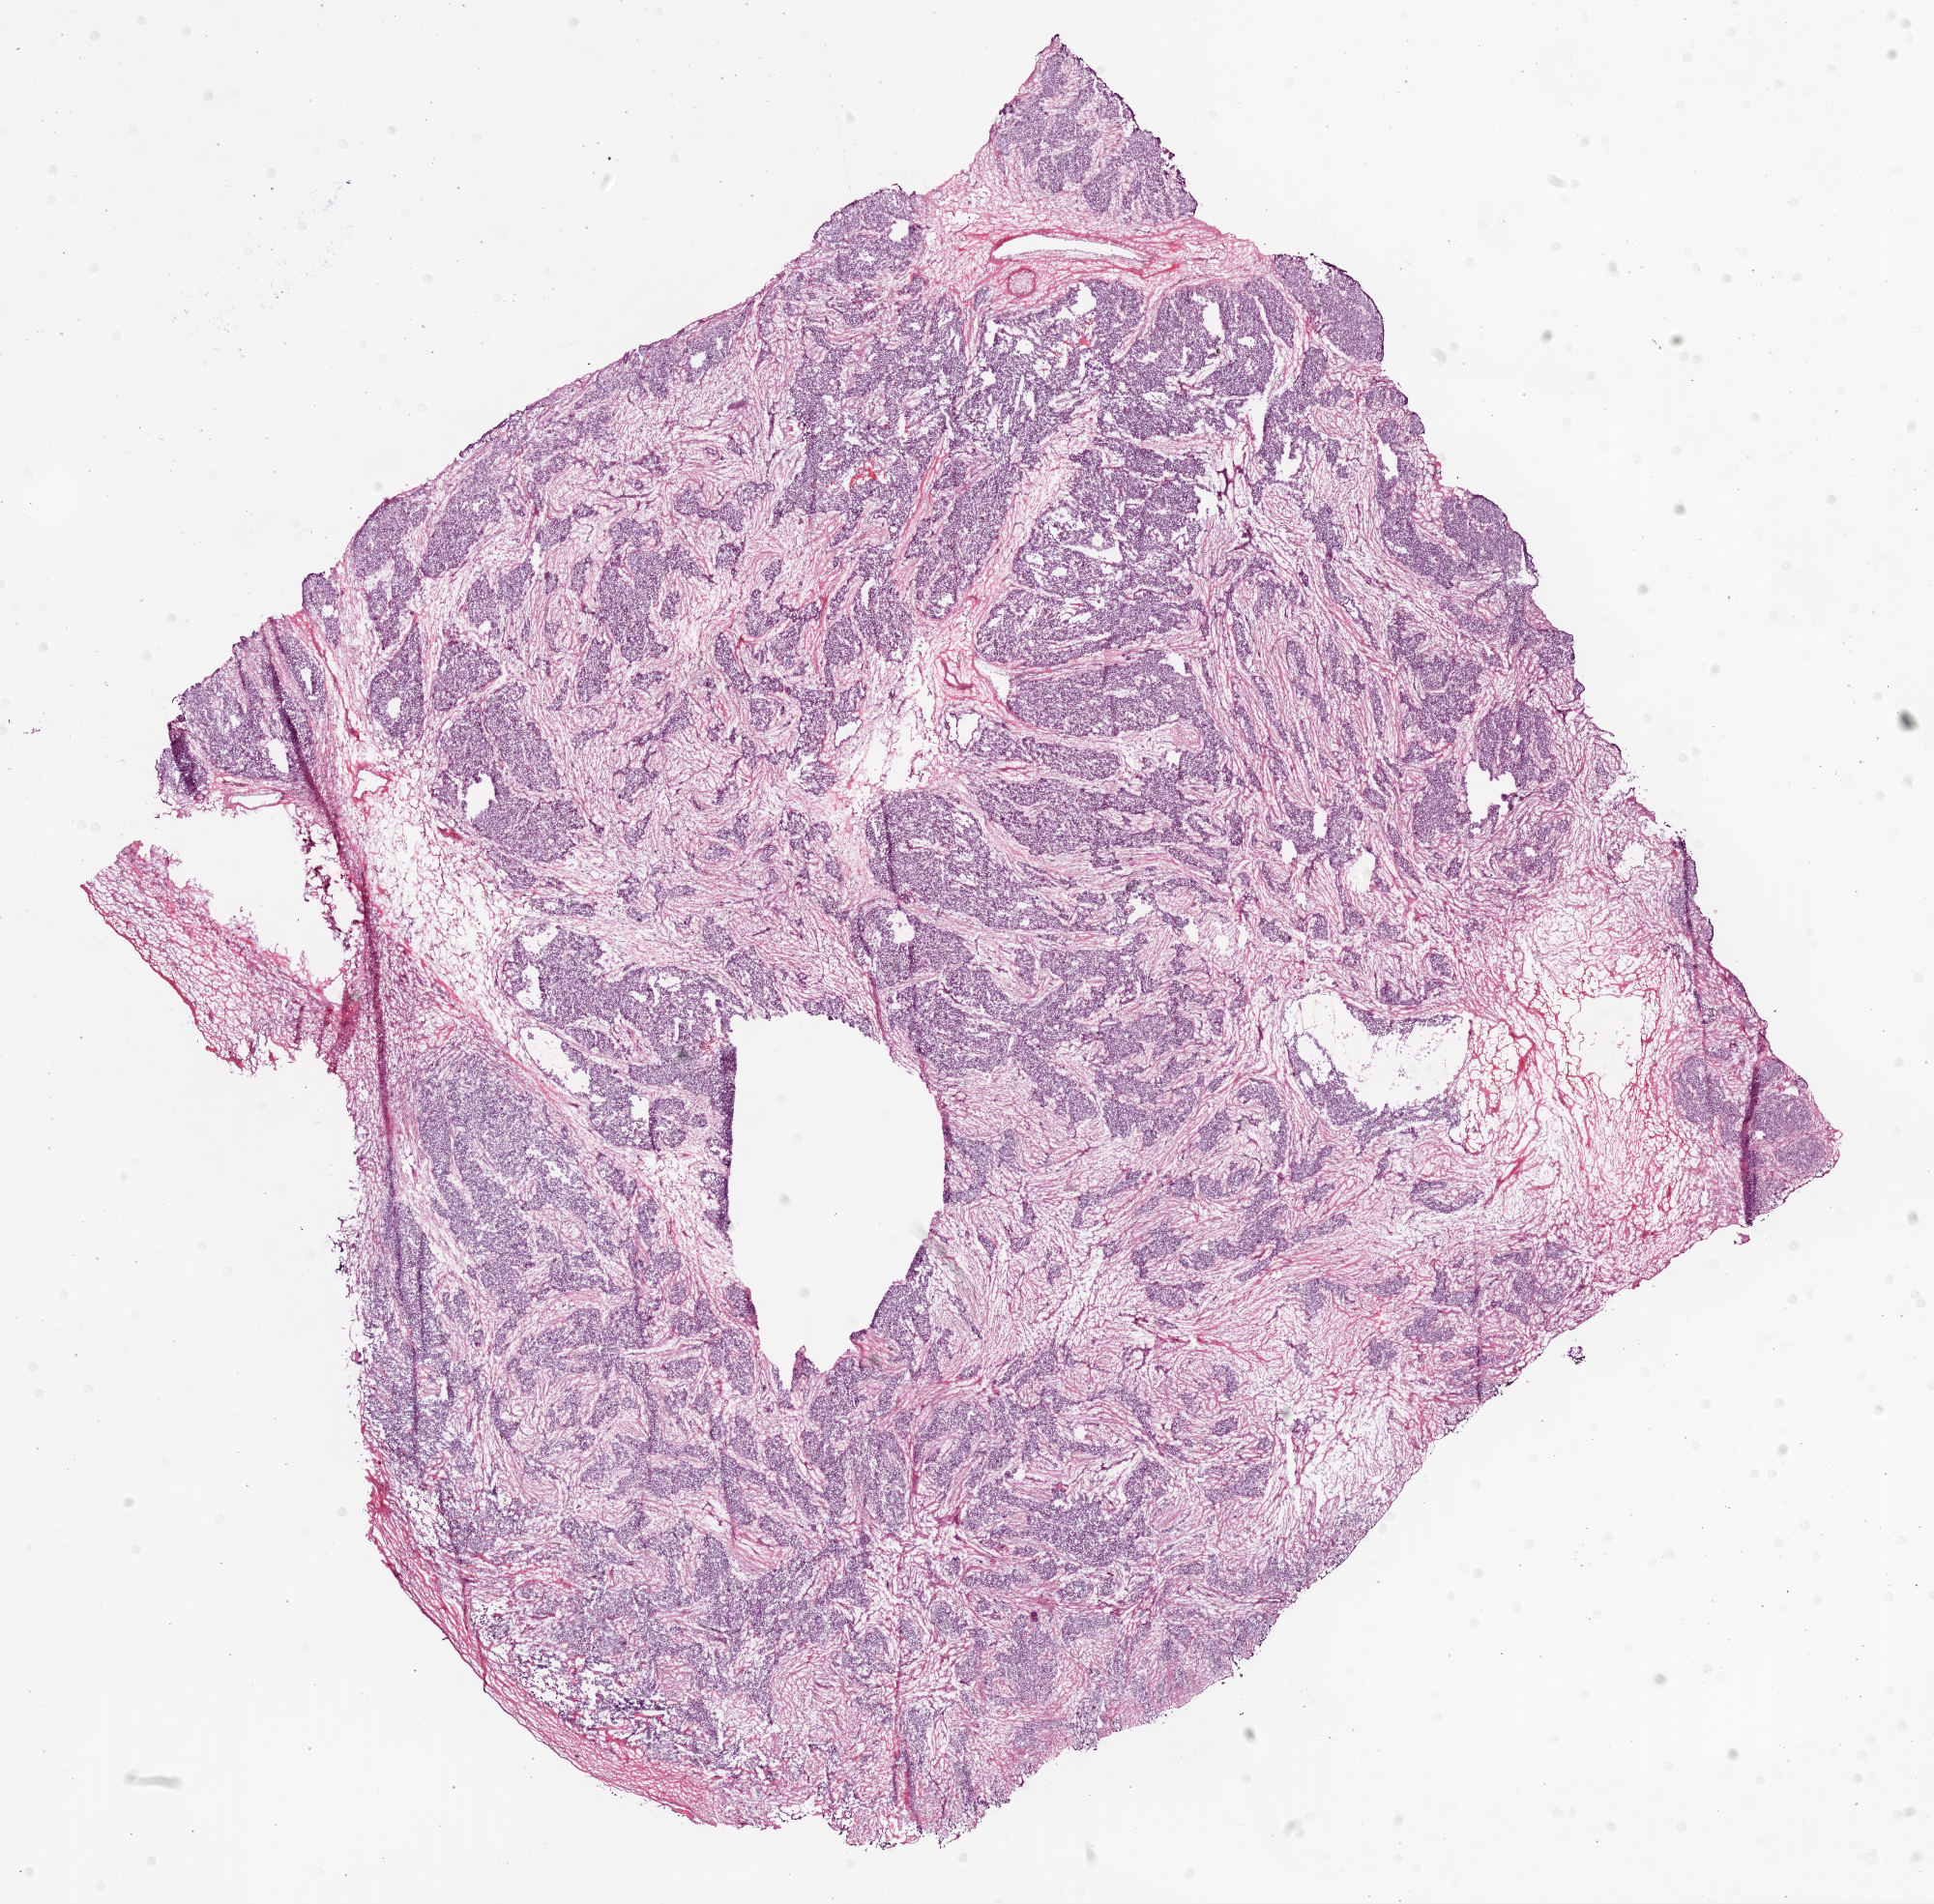
Digitized H&E tissue section (whole slide) — a low-resolution overview of the entire scanned area, about 16.0 x 15.8 mm (acquisition: 20x scan), frozen section from the bottom of the tissue portion, ovary, primary tumour sample. Patient: female, age at initial diagnosis 62 years. Histologic grade: G2 (moderately differentiated). Slide review estimates, as recorded: tumour cells 98%, tumour nuclei 85%, normal cells 0%, stromal cells 0%, necrosis 2%.
- FIGO stage: IIIC
- pathologic diagnosis: Serous cystadenocarcinoma, NOS